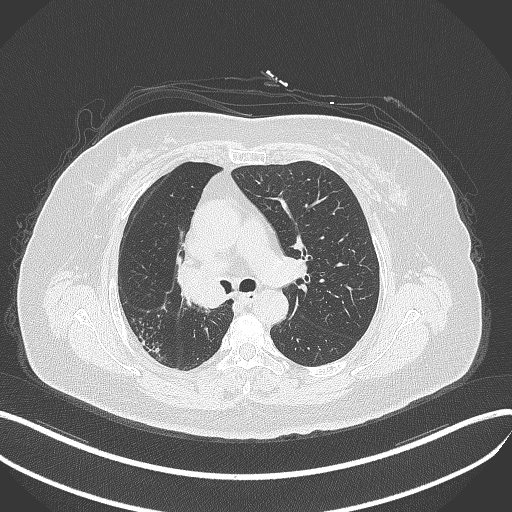
Chest CT, one axial slice; slice 229 of 376 in the series (ordered by position); reconstruction kernel B70f; 120 kVp; lung window (W 1500 / L -600 HU); 1 mm slice thickness; 512 × 512 image matrix, field of view 400 × 400 mm. Patient: female, 60 years. Case-level facts recorded for this patient, not image findings: clinical TNM (as recorded): T1c N0 M0; histopathological grade: G1-G2.
Outlined on this slice (bounding box drawn by a radiologist):
- lung tumour (recorded histology: squamous cell carcinoma): bounding box <176,261,229,312> (left, top, right, bottom; pixels)